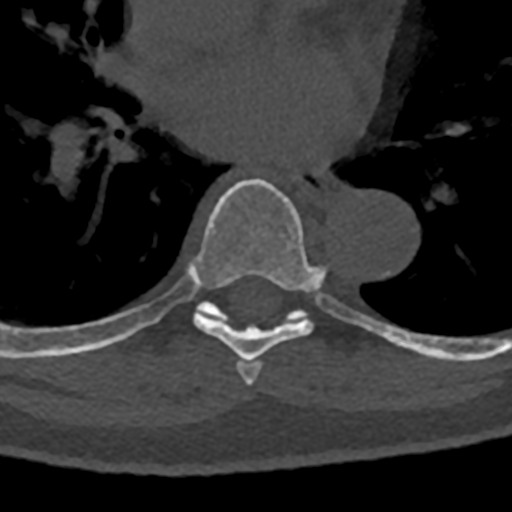
CT including the spine, one axial slice; position 752 of 797 along the scan axis; 120 kVp; bone window (W 1800 / L 400 HU); 0.5 mm slice thickness; 512 × 512 image matrix, field of view 160 × 160 mm. Male patient, age 74 years. From the clinical record (not read from this slice): primary cancer: renal; vertebrae with lytic lesions (as recorded): T10, L1, L2, L3, L4, L5.
Outlined on this slice (semi-automatically segmented with operator editing):
- T6 vertebra: bounding box <237,360,262,386> (left, top, right, bottom; pixels)
- T7 vertebra: <71,178,376,365>
- T8 vertebra: <70,303,432,358>